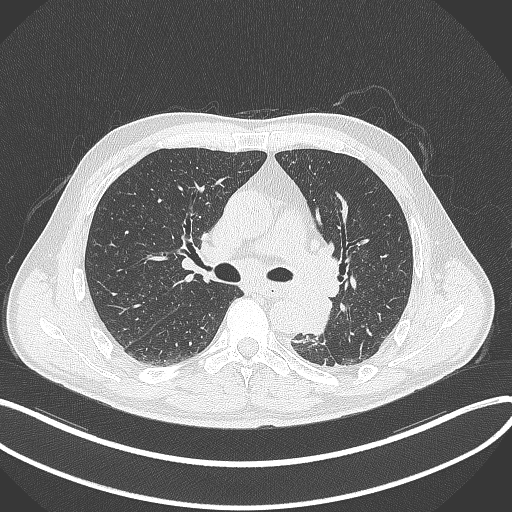
Chest CT, one axial slice; slice 209 of 329 in the series (ordered by position); reconstruction kernel B70f; 120 kVp; lung window (W 1500 / L -600 HU); 1 mm slice thickness; 512 × 512 image matrix, field of view 400 × 400 mm. Patient: male, 59 years. Case-level facts recorded for this patient, not image findings: clinical TNM (as recorded): T2a N2 M0.
Annotated regions visible in this slice (bounding box drawn by a radiologist):
- lung tumour (recorded histology: squamous cell carcinoma): box from (x=297, y=286) to (x=331, y=335) px